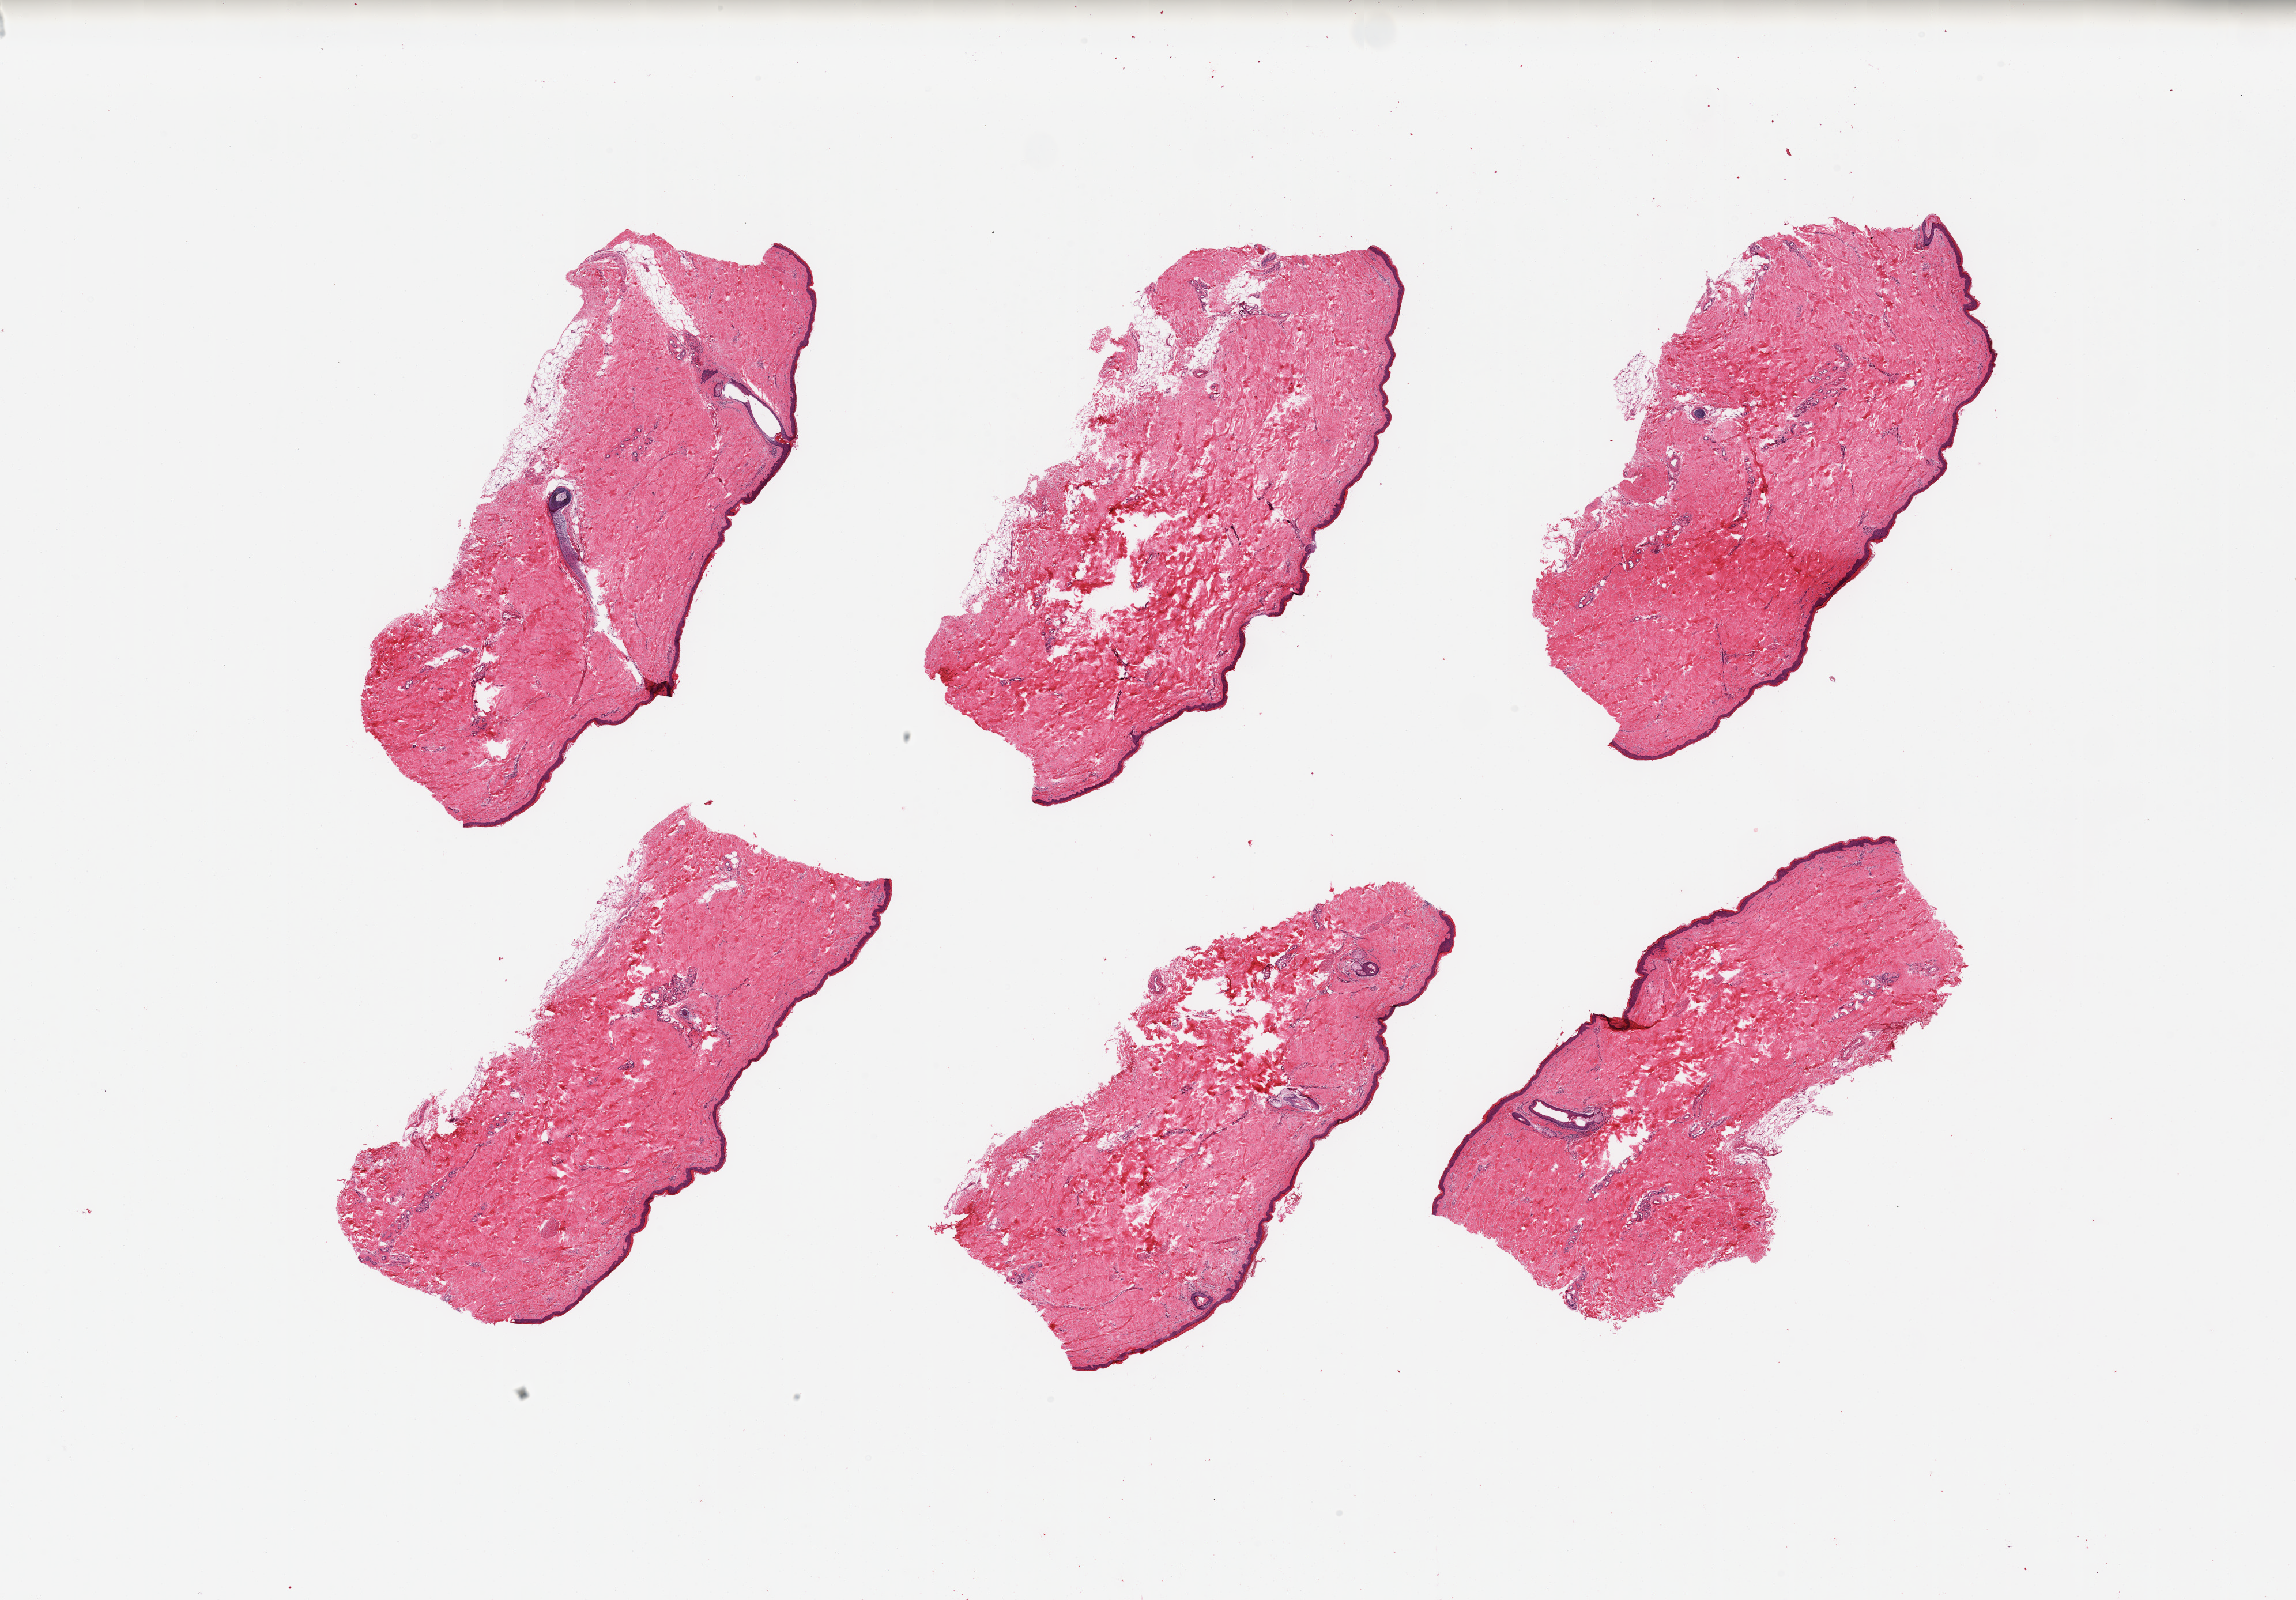
Digitized haematoxylin and eosin-stained section, brightfield — whole scanned area (about 31.5 x 22.0 mm, from a 20x scan) shown as a low-resolution overview. PAXgene-fixed, paraffin-embedded tissue. Sampled site (target tissue): skin of lower leg. Donor tissue sample. Donor sex: male.
Reviewer comment on this tissue sample: 6 pieces; well dissected; 5% dermal fat.